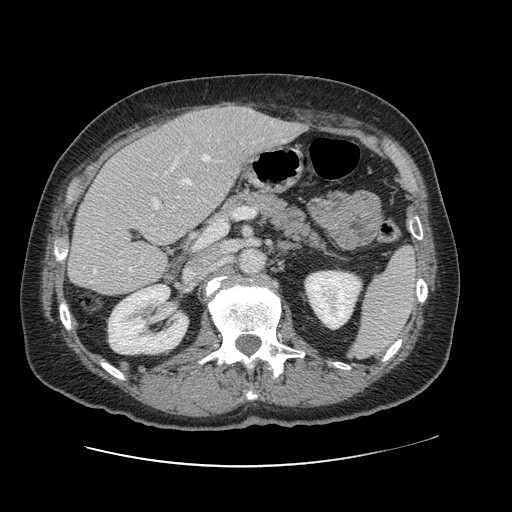
Contrast-enhanced abdominal CT, one axial slice. 120 kVp. Intravenous contrast given. Soft-tissue window (W 400 / L 40 HU). 2.5 mm slice thickness. 512 × 512 image matrix. Male patient, age 71 years. From the clinical record (not read from this slice): diagnosis: colorectal cancer liver metastases, imaged before liver resection.
Outlined on this slice (outlined manually by an expert reader):
- hepatic veins: box from (x=93, y=155) to (x=227, y=274) px
- liver: (x=70, y=106)–(x=300, y=295)
- planned liver remnant (the part of the liver to remain after resection): (x=70, y=142)–(x=199, y=294)
- portal vein (with intrahepatic branches): (x=152, y=172)–(x=167, y=209)